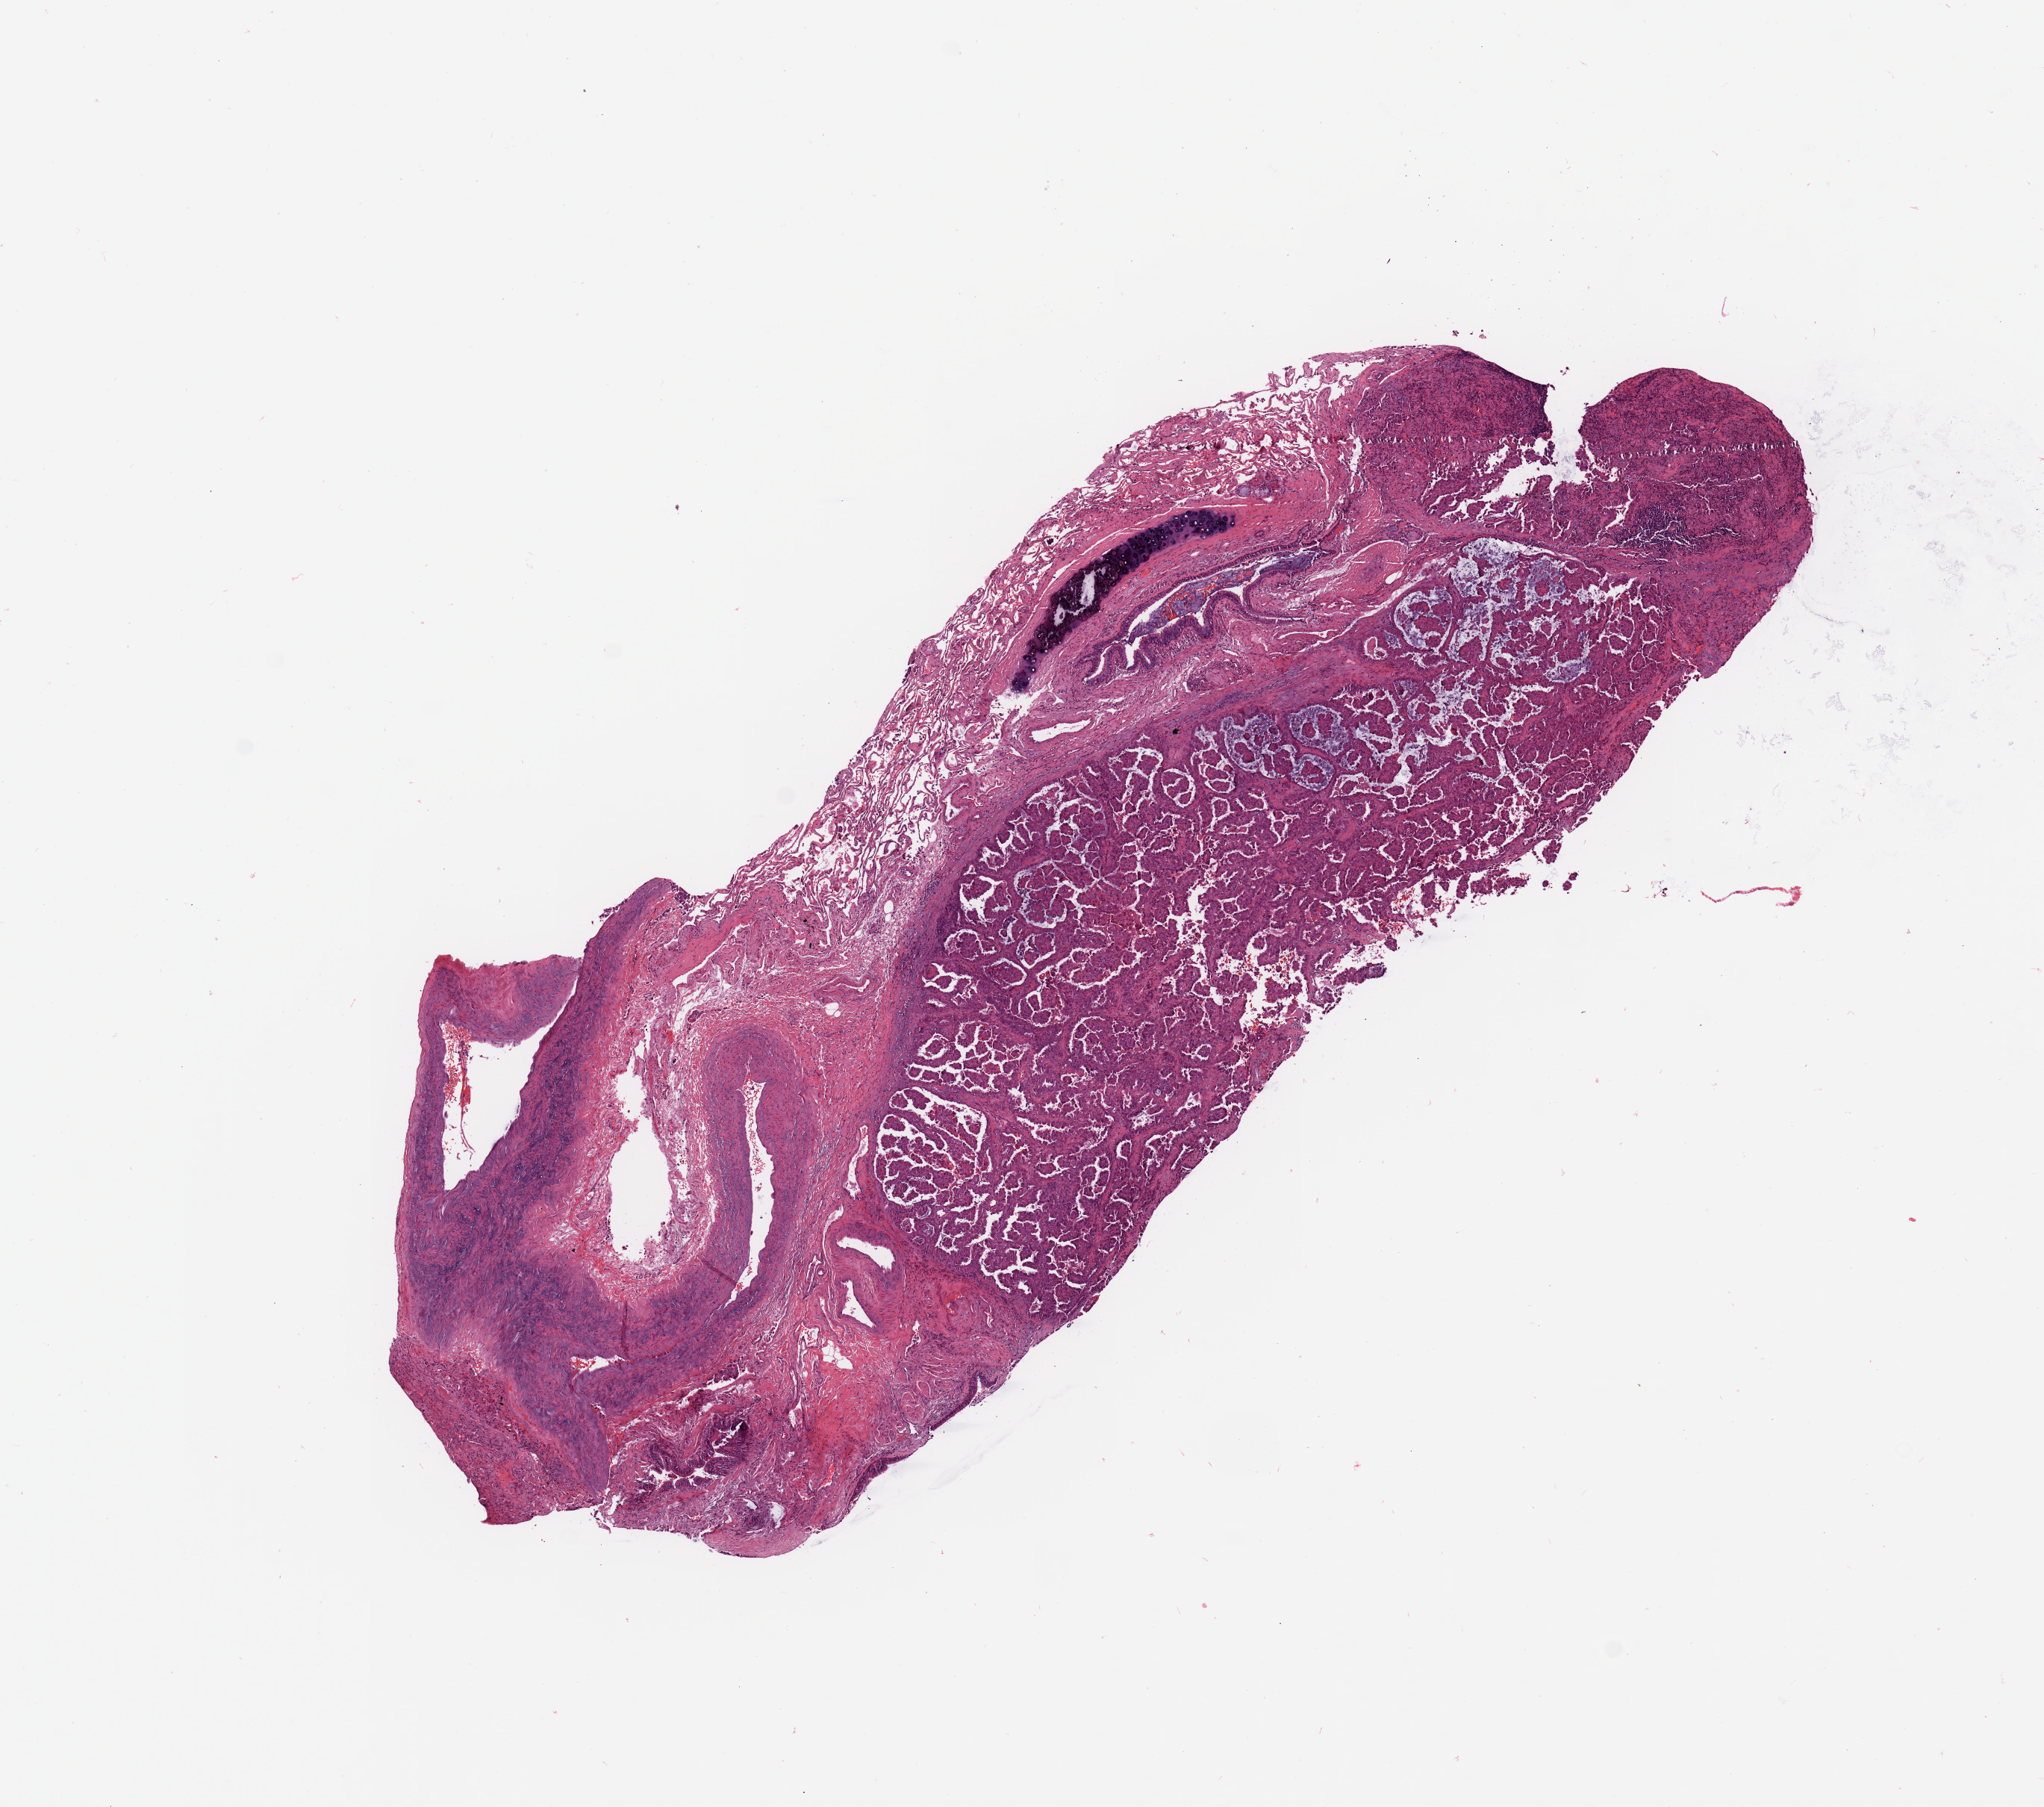
Whole-slide histology image, H&E-stained, shown as a low-resolution overview of the whole scanned area (about 10.8 x 9.6 mm, slide scanned at 20x), tumour tissue sample, lung. Male, 77 y/o. Histologic grade: G2 (moderately differentiated).
Diagnosis: Adenocarcinoma, NOS. AJCC pathologic stage: IIA.